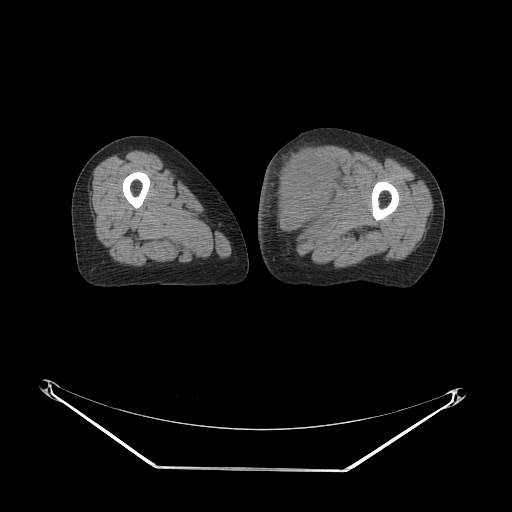
CT of an extremity soft-tissue mass (from a PET/CT study), one axial slice; slice 40 of 91 in the series (ordered by position); 140 kVp; soft-tissue window (W 400 / L 40 HU); 3.75 mm slice thickness; 512 × 512 image matrix, field of view 500 × 500 mm. Female patient. Case-level facts recorded for this patient, not image findings: histological type: pleomorphic leiomyosarcoma; grade: high; site of the primary tumour: left thigh.
Annotated regions visible in this slice (expert contour drawn on MRI and transferred to this co-registered scan by the dataset authors):
- gross tumour volume including surrounding oedema: box from (x=267, y=144) to (x=344, y=238) px
- gross tumour volume (mass): (x=274, y=144)–(x=343, y=227)